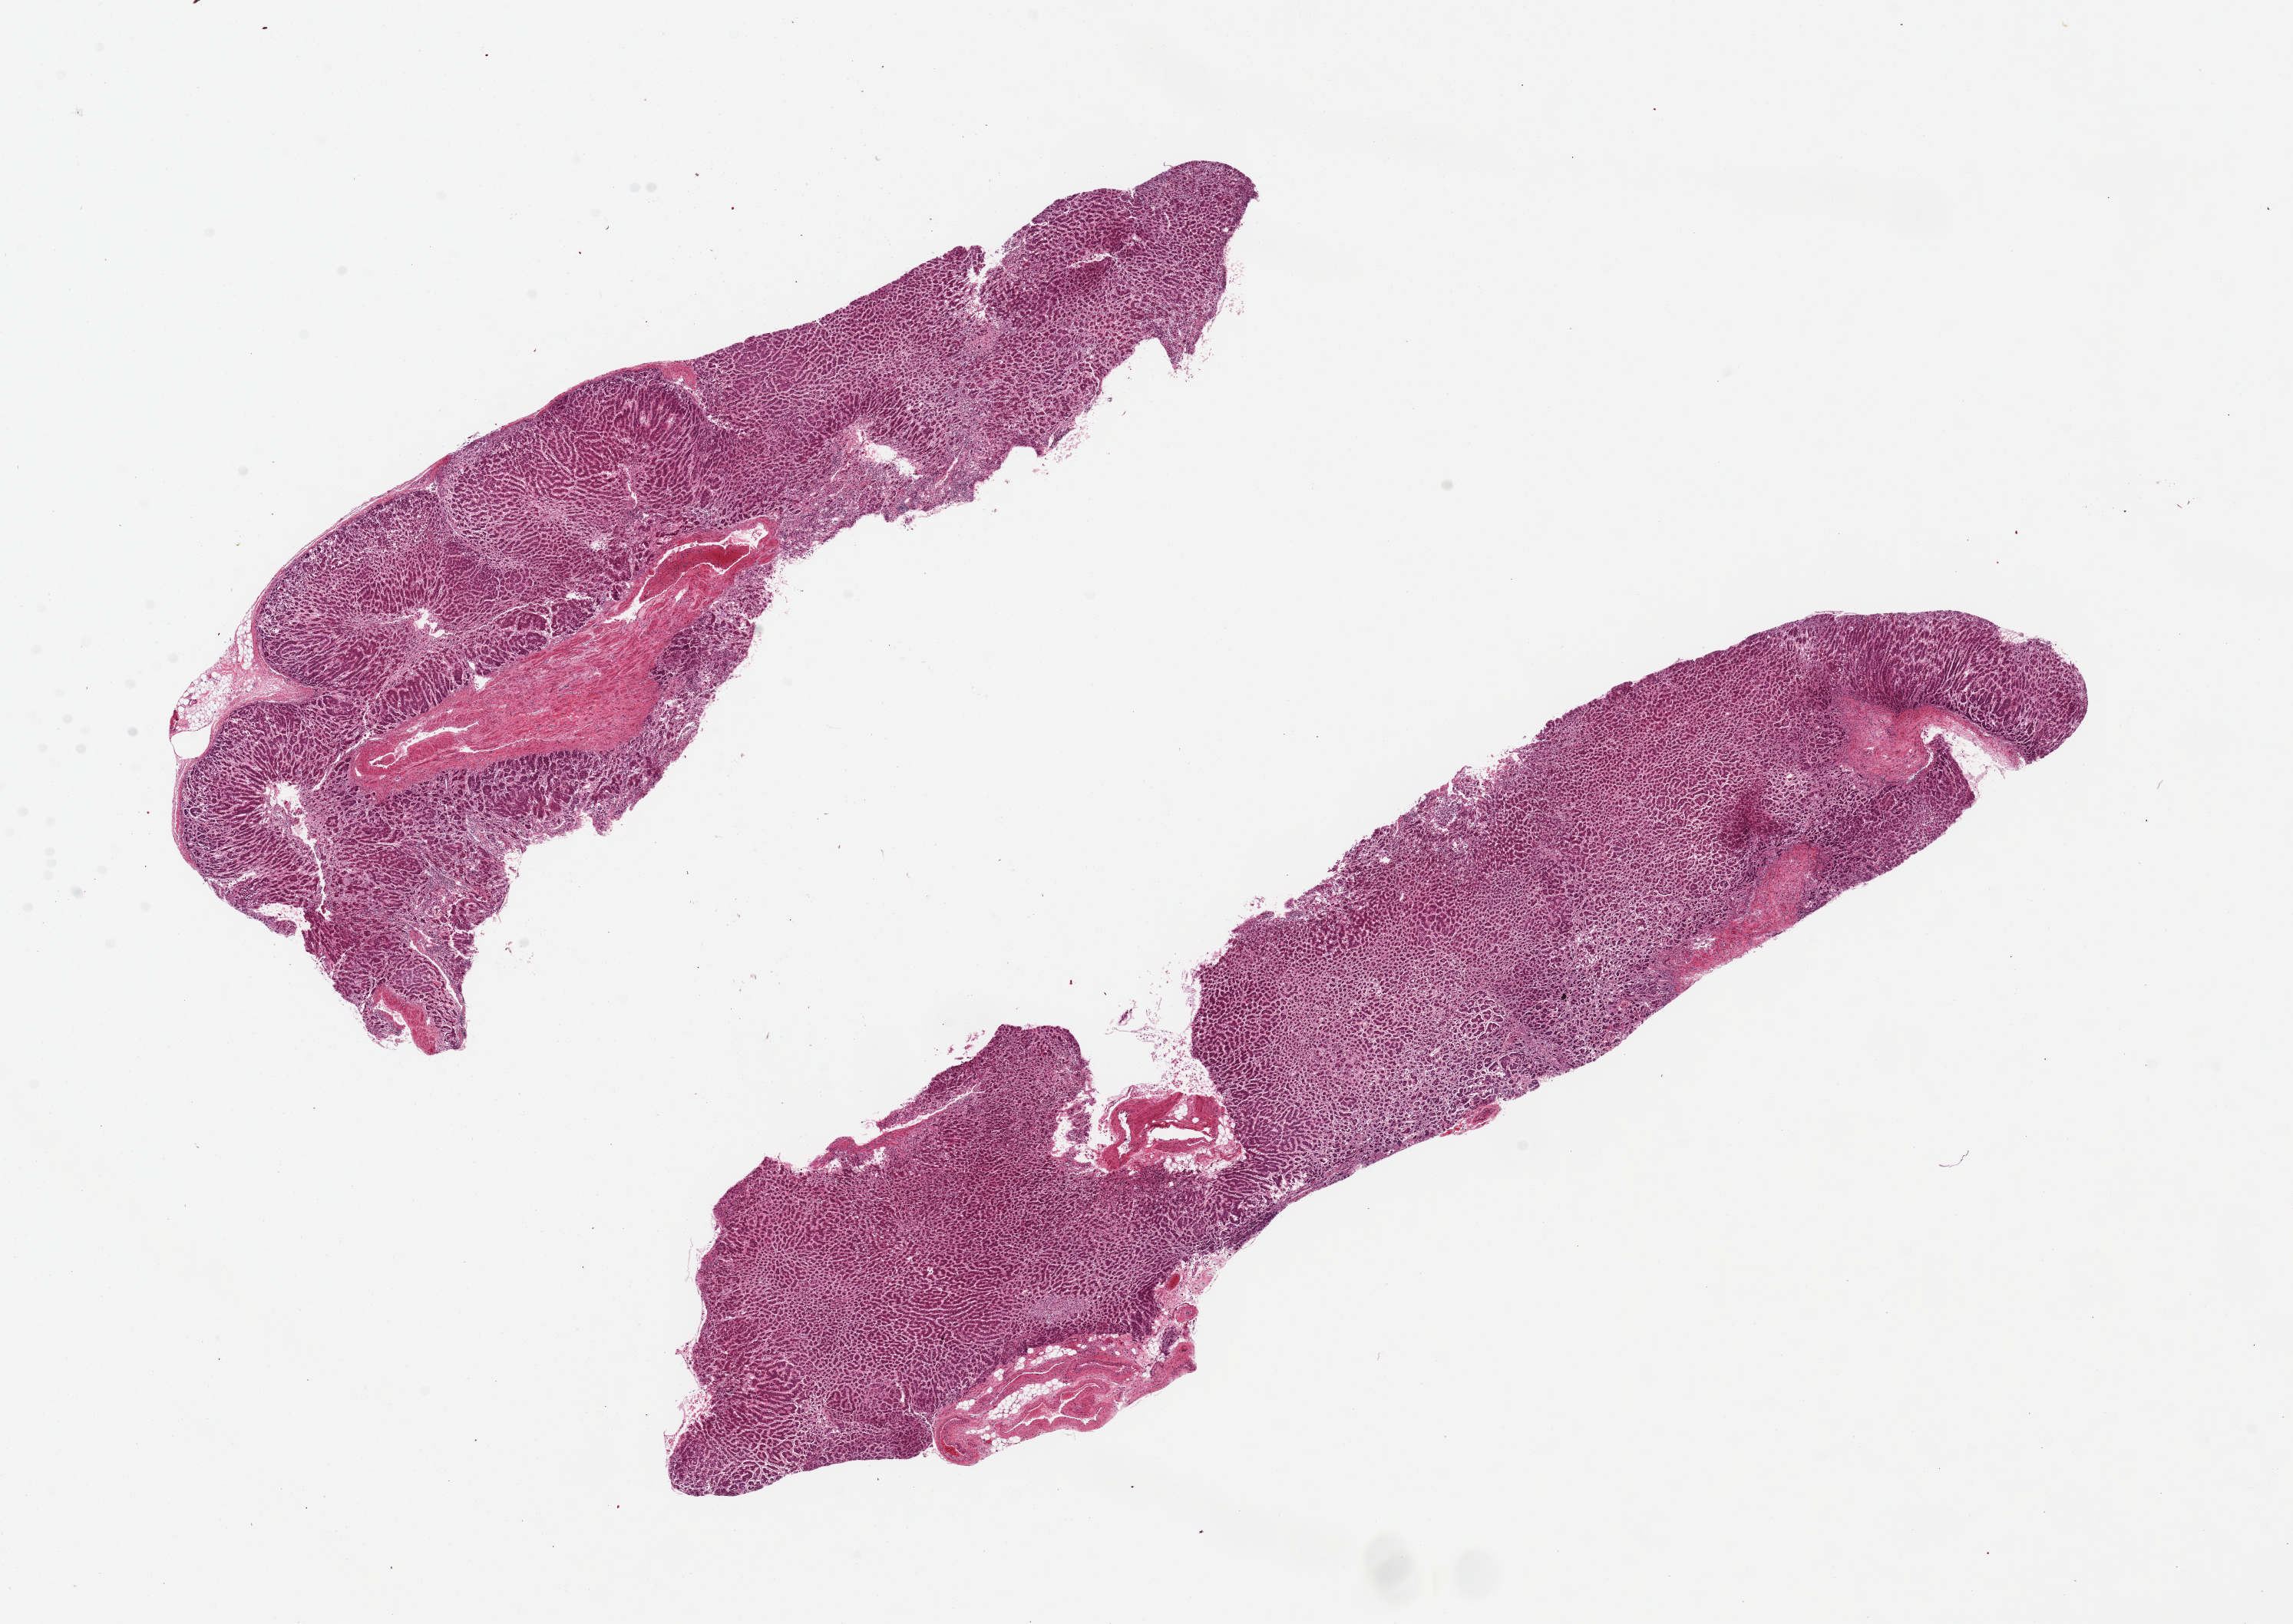
Digitized haematoxylin and eosin-stained section, brightfield — low-resolution overview of the scanned area, about 23.6 x 16.7 mm (acquisition: 20x scan); PAXgene-fixed, paraffin-embedded tissue; sampled site (target tissue): adrenal gland; tissue donor sample. Donor: female.
Reviewer comment on this tissue sample: 2 pieces 14x3mm, all cortex, moderately autolyzed.